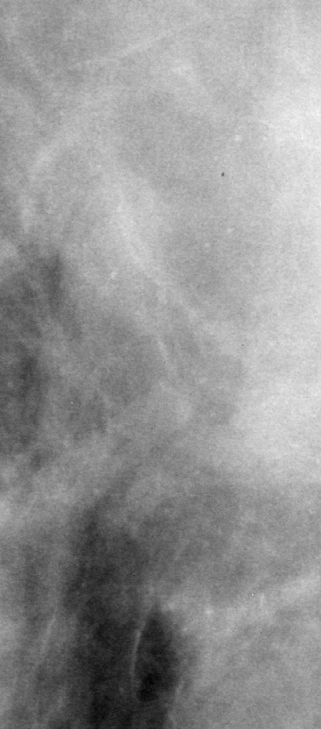
Crop from a digitized film mammogram around one marked abnormality; left breast; CC view.
Marked abnormality: calcifications, morphology pleomorphic, distribution regional; BI-RADS assessment category 4; subtlety rating 2 on a 1 (subtle) to 5 (obvious) scale; pathology result (as recorded, not read from the image): malignant.